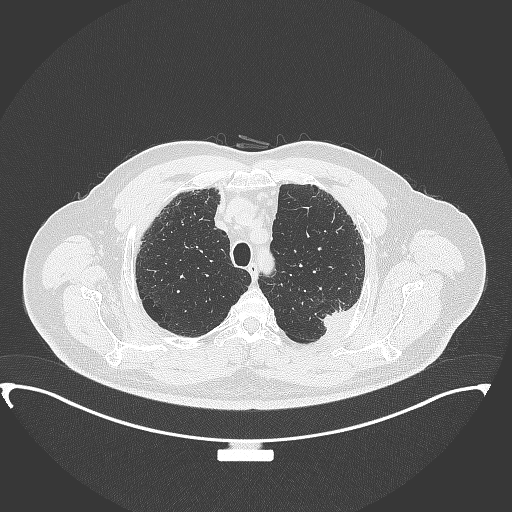
Chest CT, one axial slice. Position 292 of 350 along the scan axis. Reconstruction kernel B70f. 120 kVp. Lung window (W 1500 / L -600 HU). 1 mm slice thickness. 512 × 512 image matrix, field of view 459 × 459 mm. Male patient, age 64 years. From the clinical record (not read from this slice): clinical TNM (as recorded): T1c N1 M1.
Annotated regions visible in this slice (rectangle marked by the reading radiologist):
- lung tumour (recorded histology: adenocarcinoma): bounding box <318,305,349,329> (left, top, right, bottom; pixels)